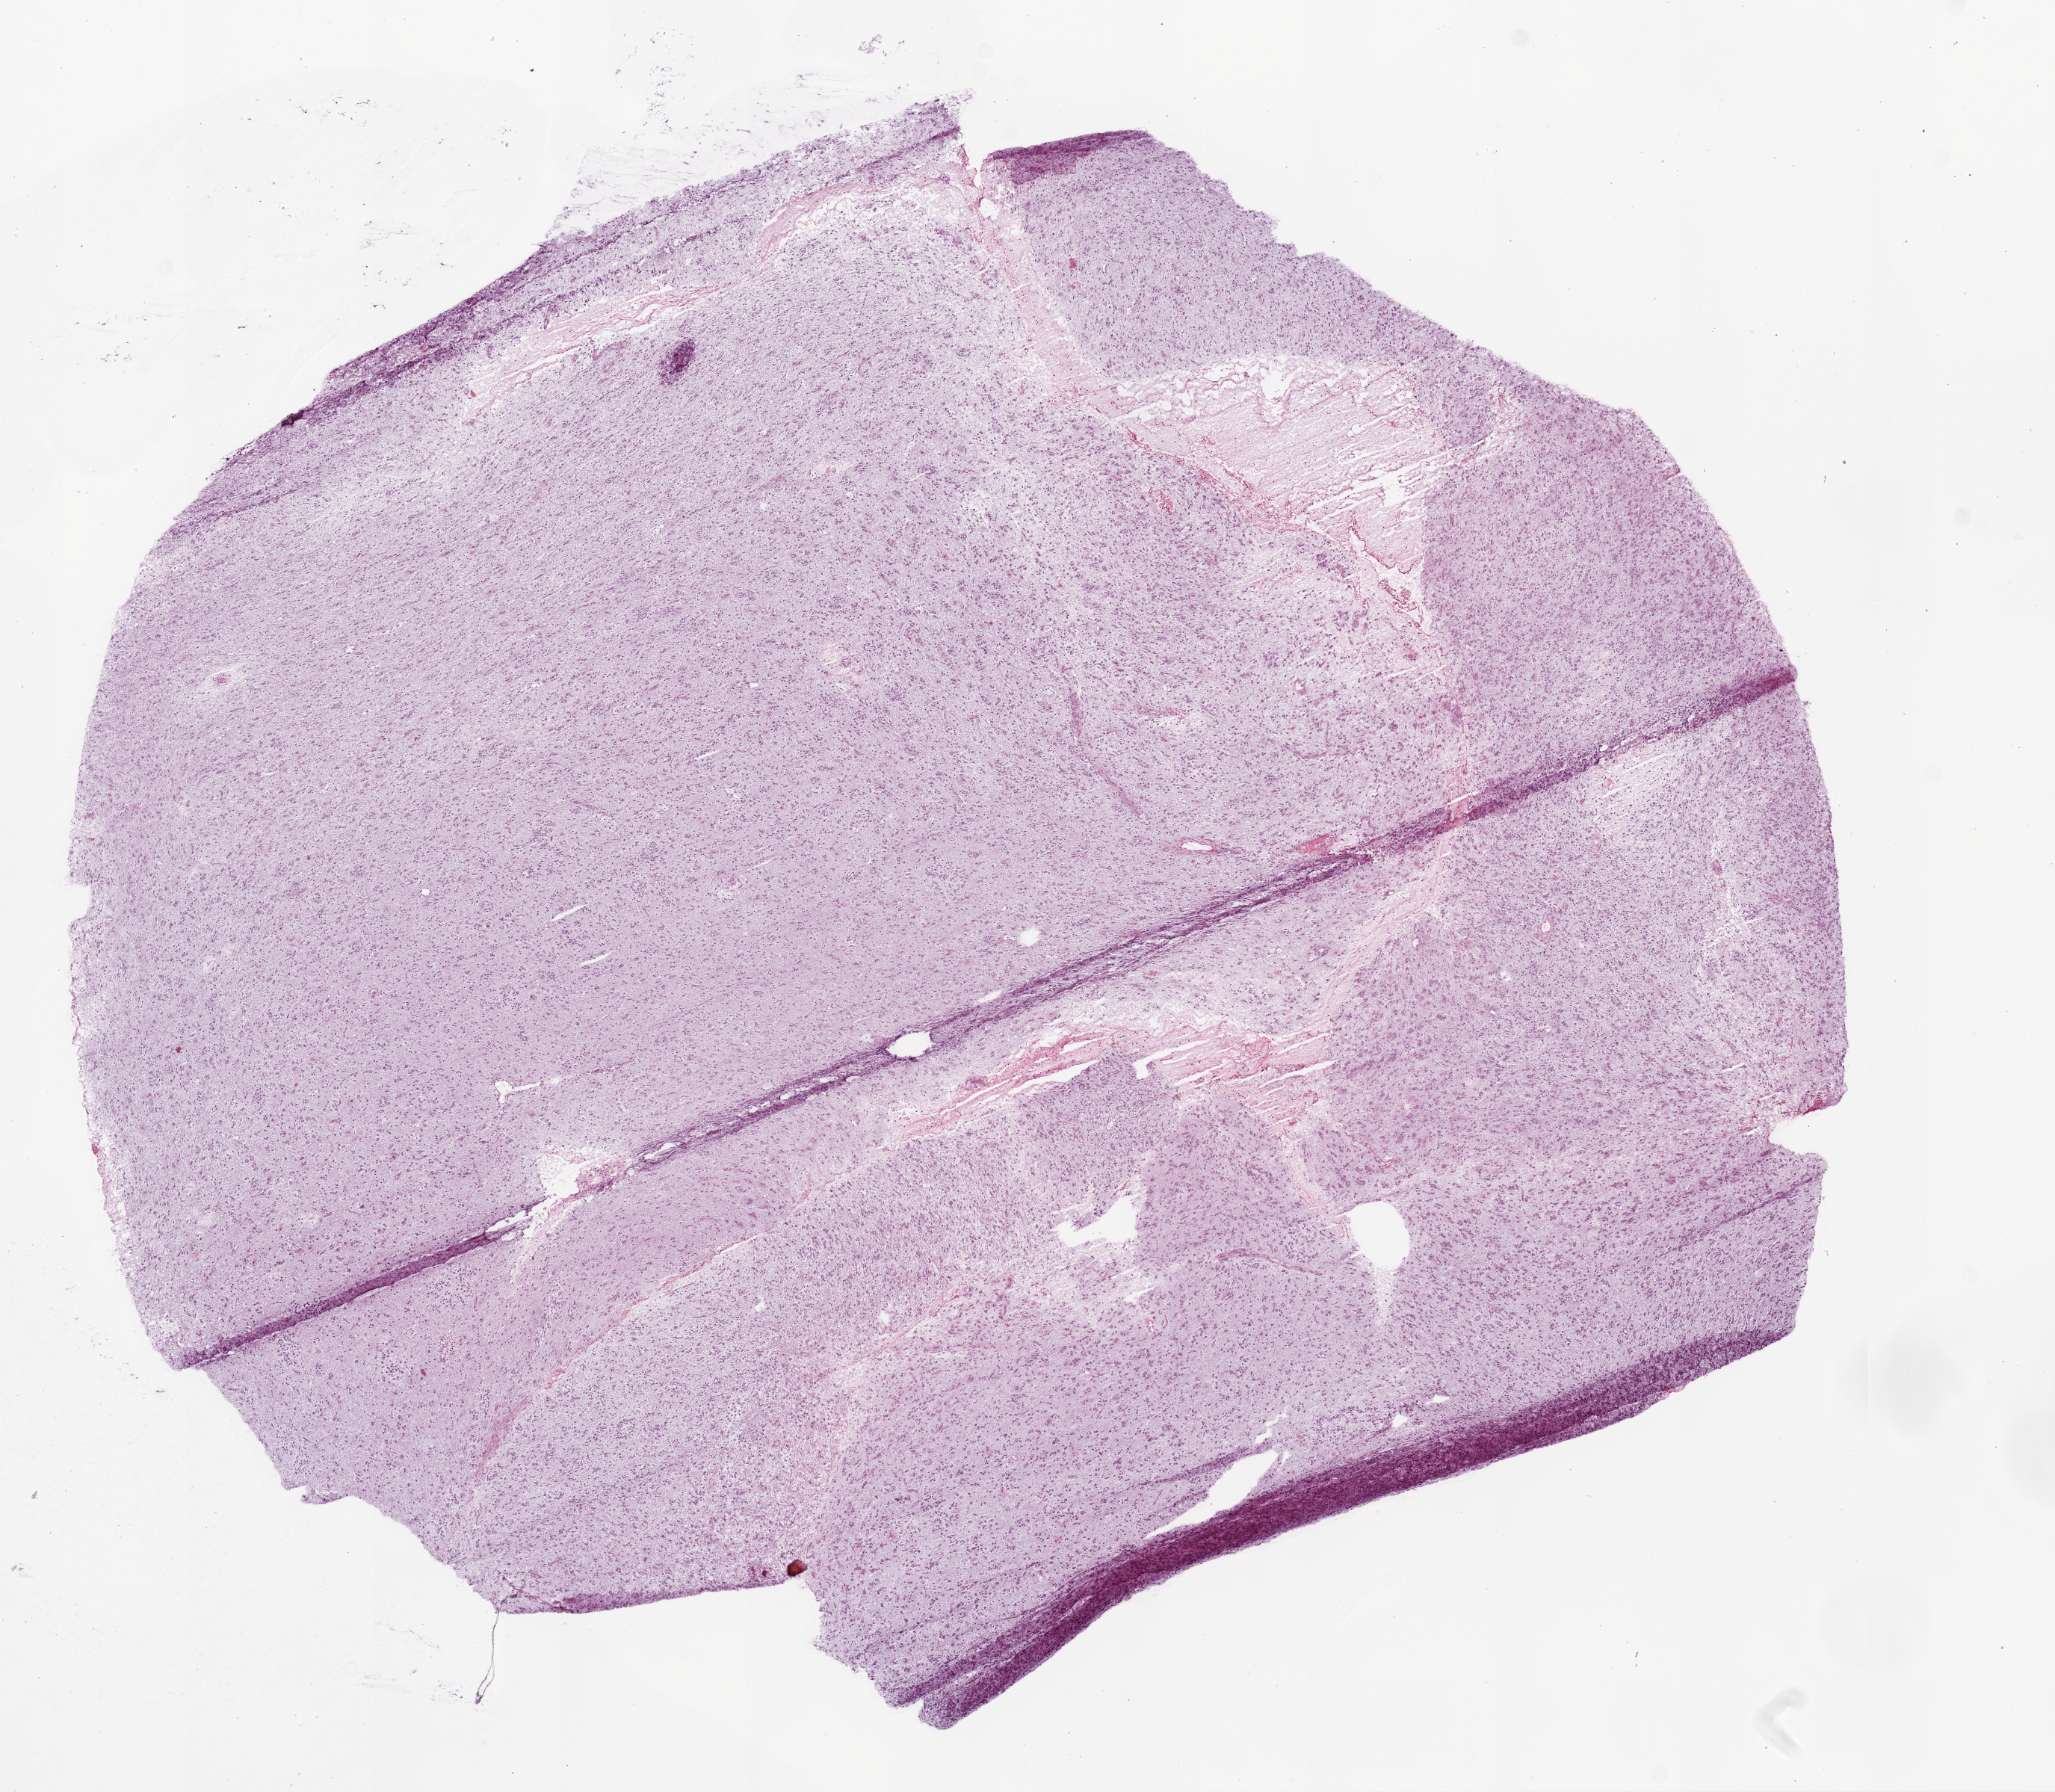
Digitized Hematoxylin and eosin (H&E) stained tissue section (whole slide) — low-resolution overview of the scanned area, about 11.0 x 9.6 mm (from a 20x scan). Frozen section. Brain, primary tumour sample. Patient: female, age at initial diagnosis 81 years. Slide review estimates, as recorded: tumour cells 70%, tumour nuclei 75%, normal cells 20%, stromal cells 5%, necrosis 5%.
Histologic diagnosis: Glioblastoma.